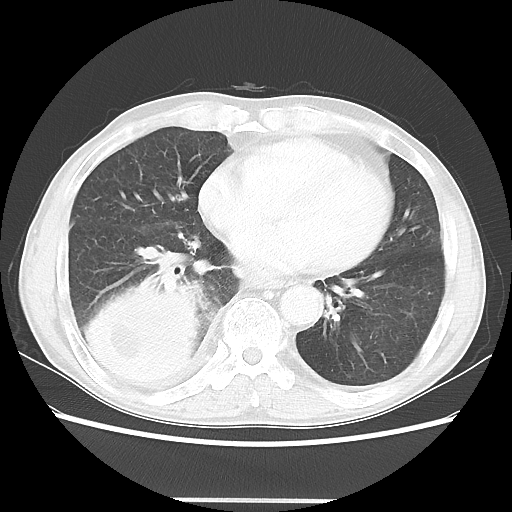
Chest CT, one axial slice. Slice 16 of 48 in the series (ordered by position). Reconstruction kernel LUNG. 100 kVp. Lung window (W 1500 / L -600 HU). 5 mm slice thickness. 512 × 512 image matrix, field of view 361 × 361 mm. Male patient, age 66 years. From the clinical record (not read from this slice): clinical TNM (as recorded): T4 N1 M1; histopathological grade: G3.
Outlined on this slice (bounding box drawn by a radiologist):
- lung tumour (recorded histology: small cell carcinoma): bounding box <73,270,206,396> (left, top, right, bottom; pixels)